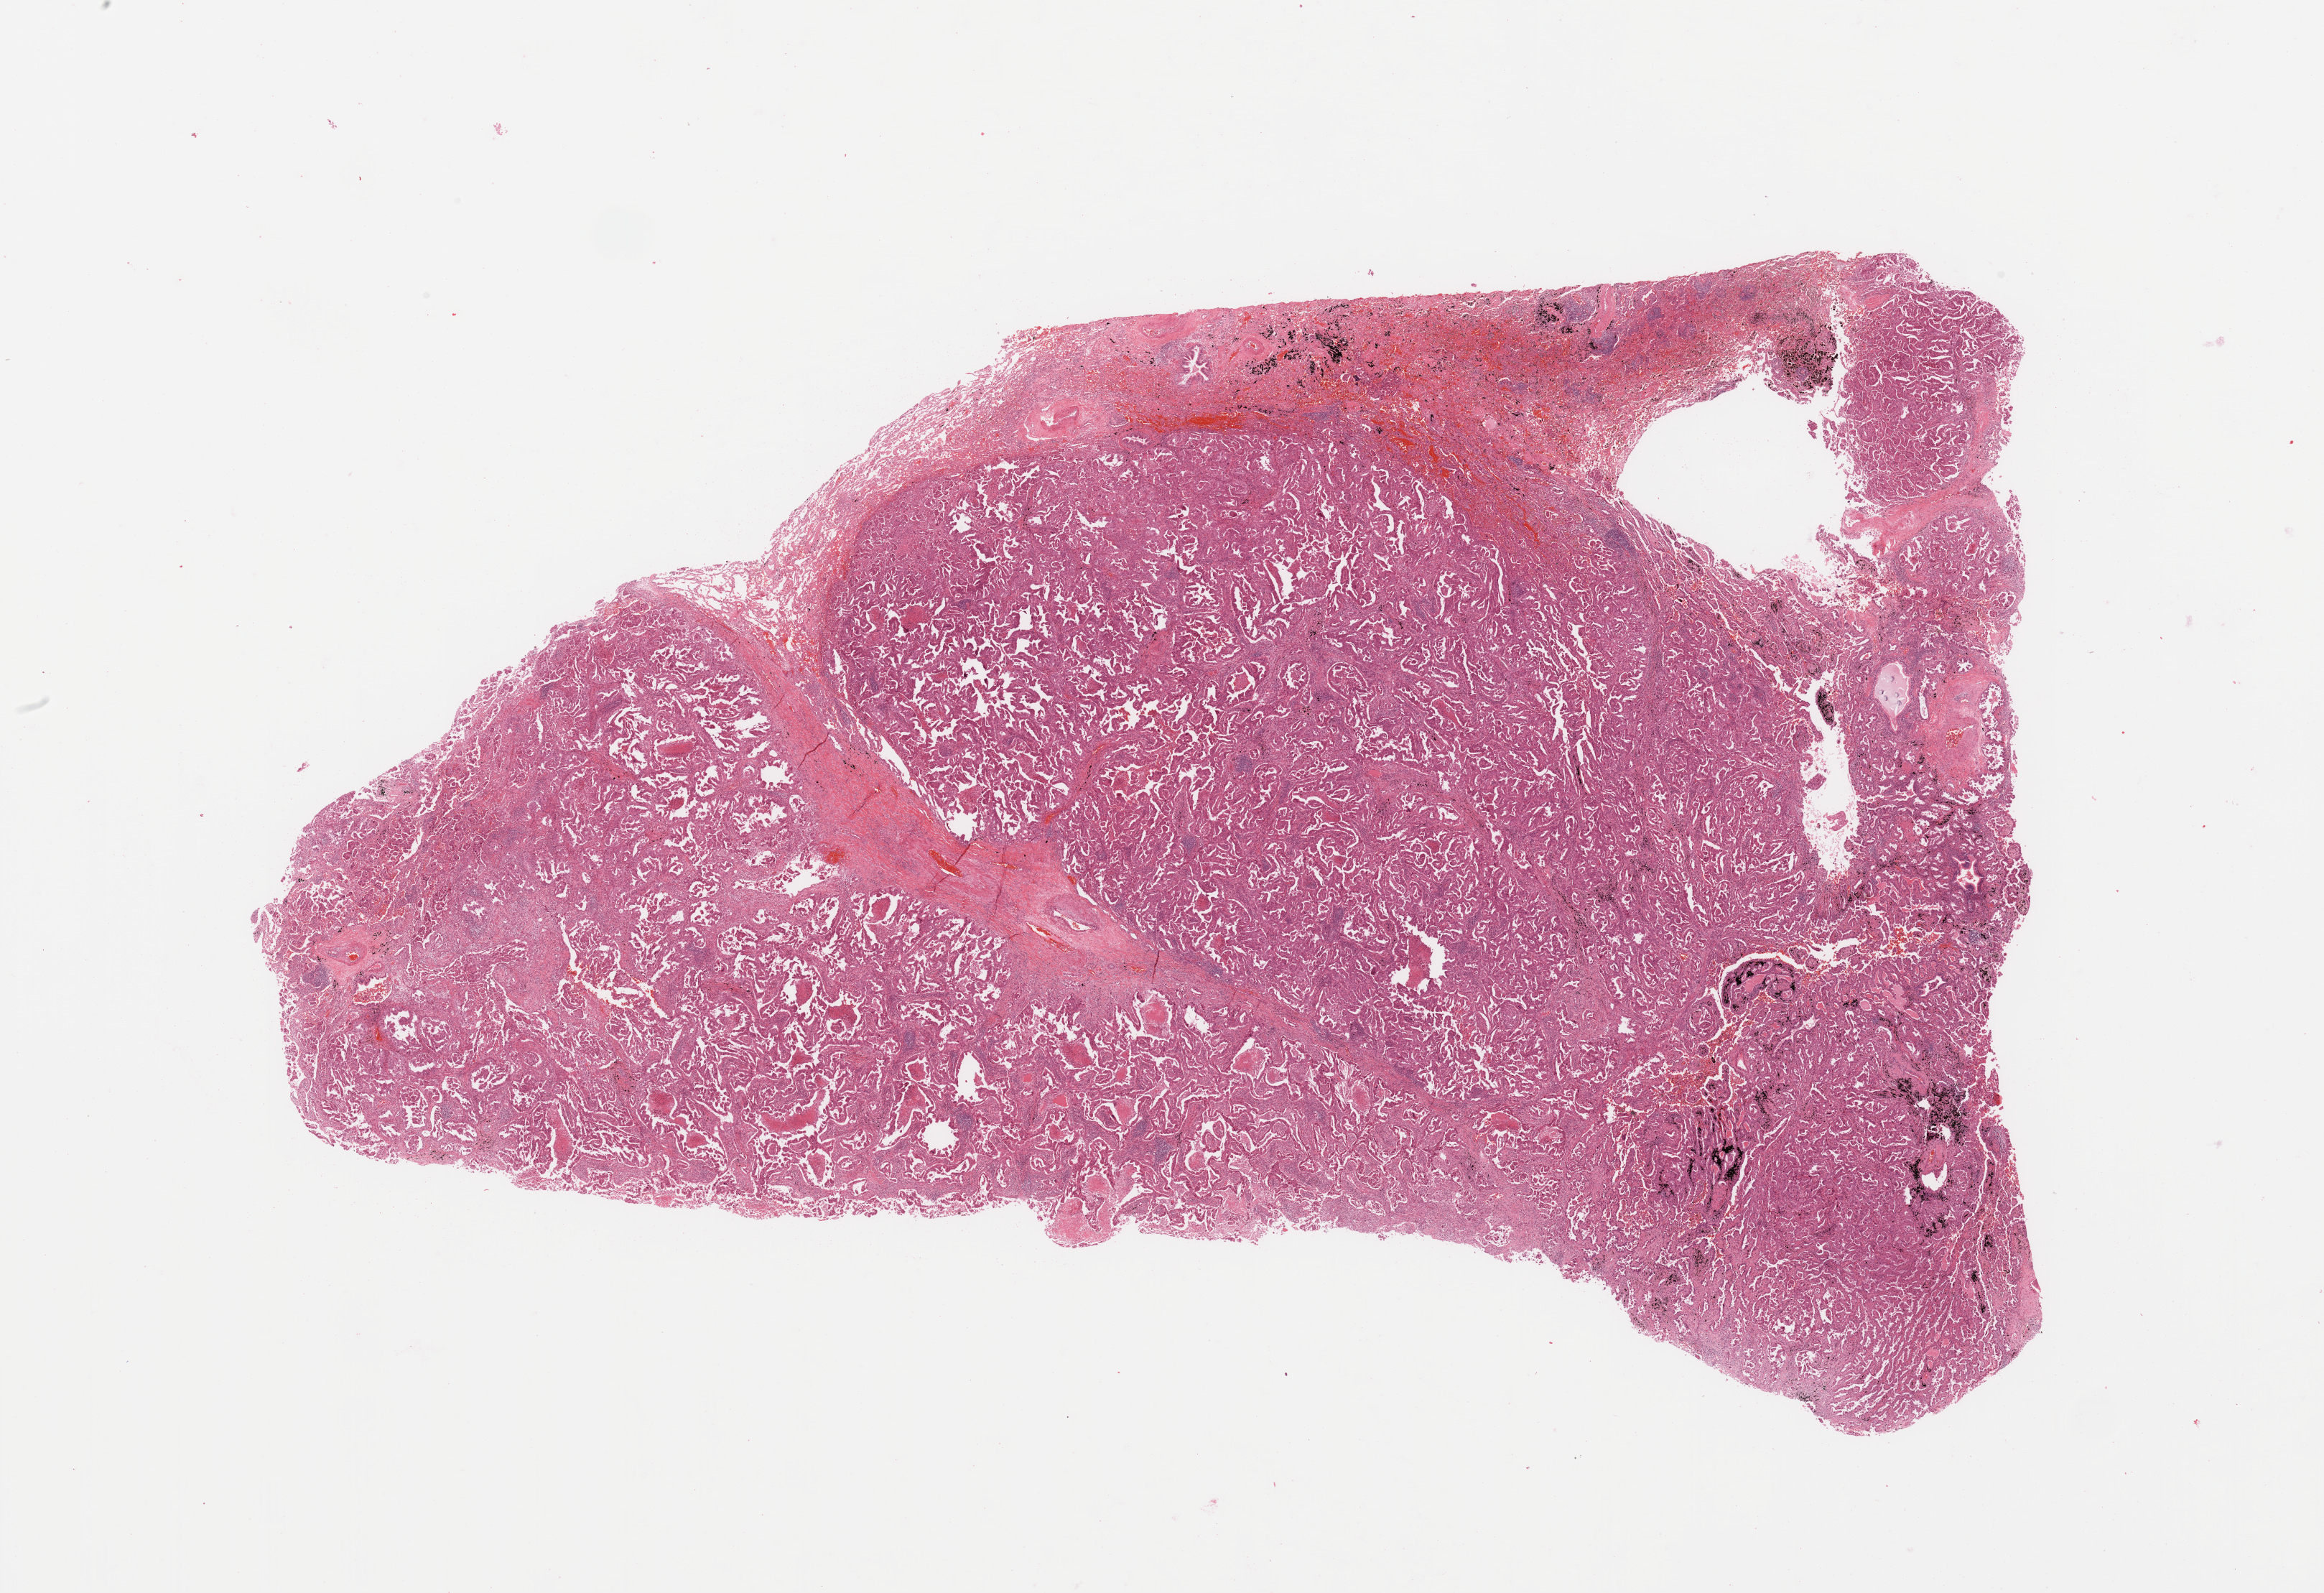
Hematoxylin and eosin (H&E) stained whole-slide image, shown as a low-resolution overview of the whole scanned area (about 25.6 x 17.5 mm). Tumour tissue sample, lung. 72-year-old male patient. Histologic grade: G2 (moderately differentiated).
Diagnosis: Adenocarcinoma, NOS. AJCC pathologic stage: IB.